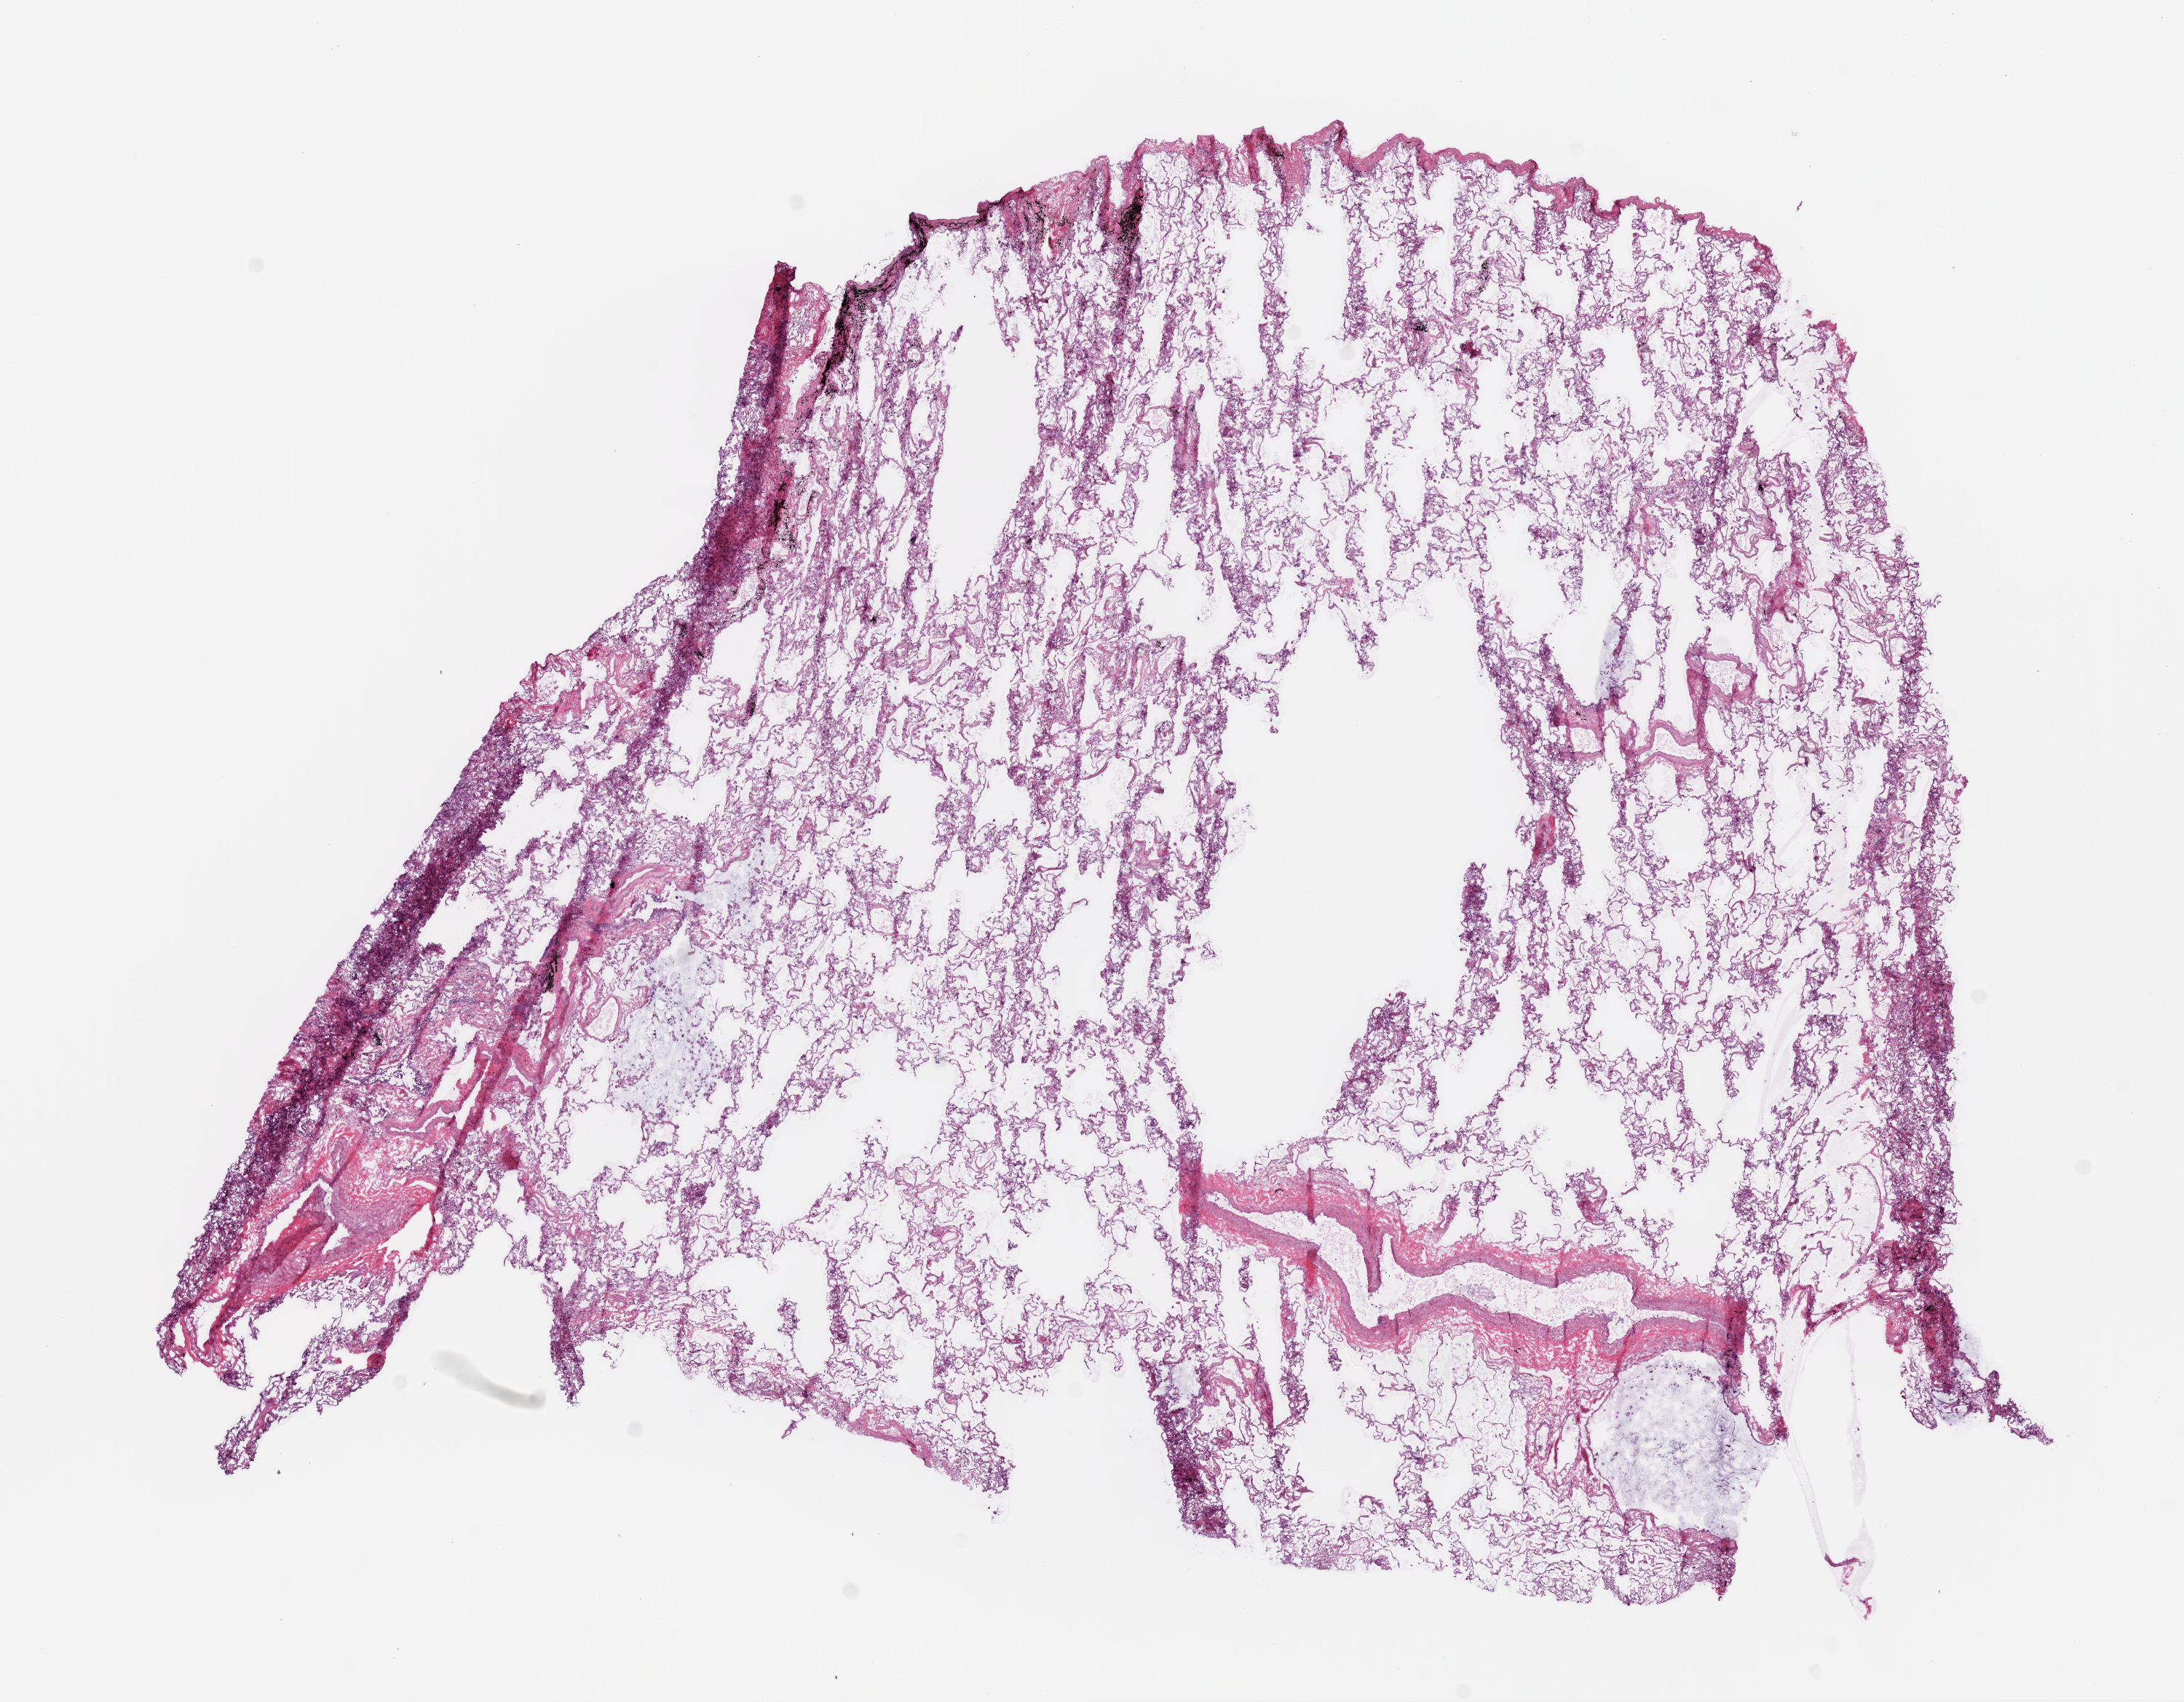
H&E whole-slide image — a low-resolution overview of the entire scanned area, about 12.0 x 9.4 mm. Frozen section from the bottom of the tissue portion. Solid tissue normal (non-tumour tissue) sample from the lung. Male patient; age at initial diagnosis 74 years.
- this section: solid tissue normal sample (biorepository sample class)
- patient diagnosis: Squamous cell carcinoma, NOS (upper lobe, lung)